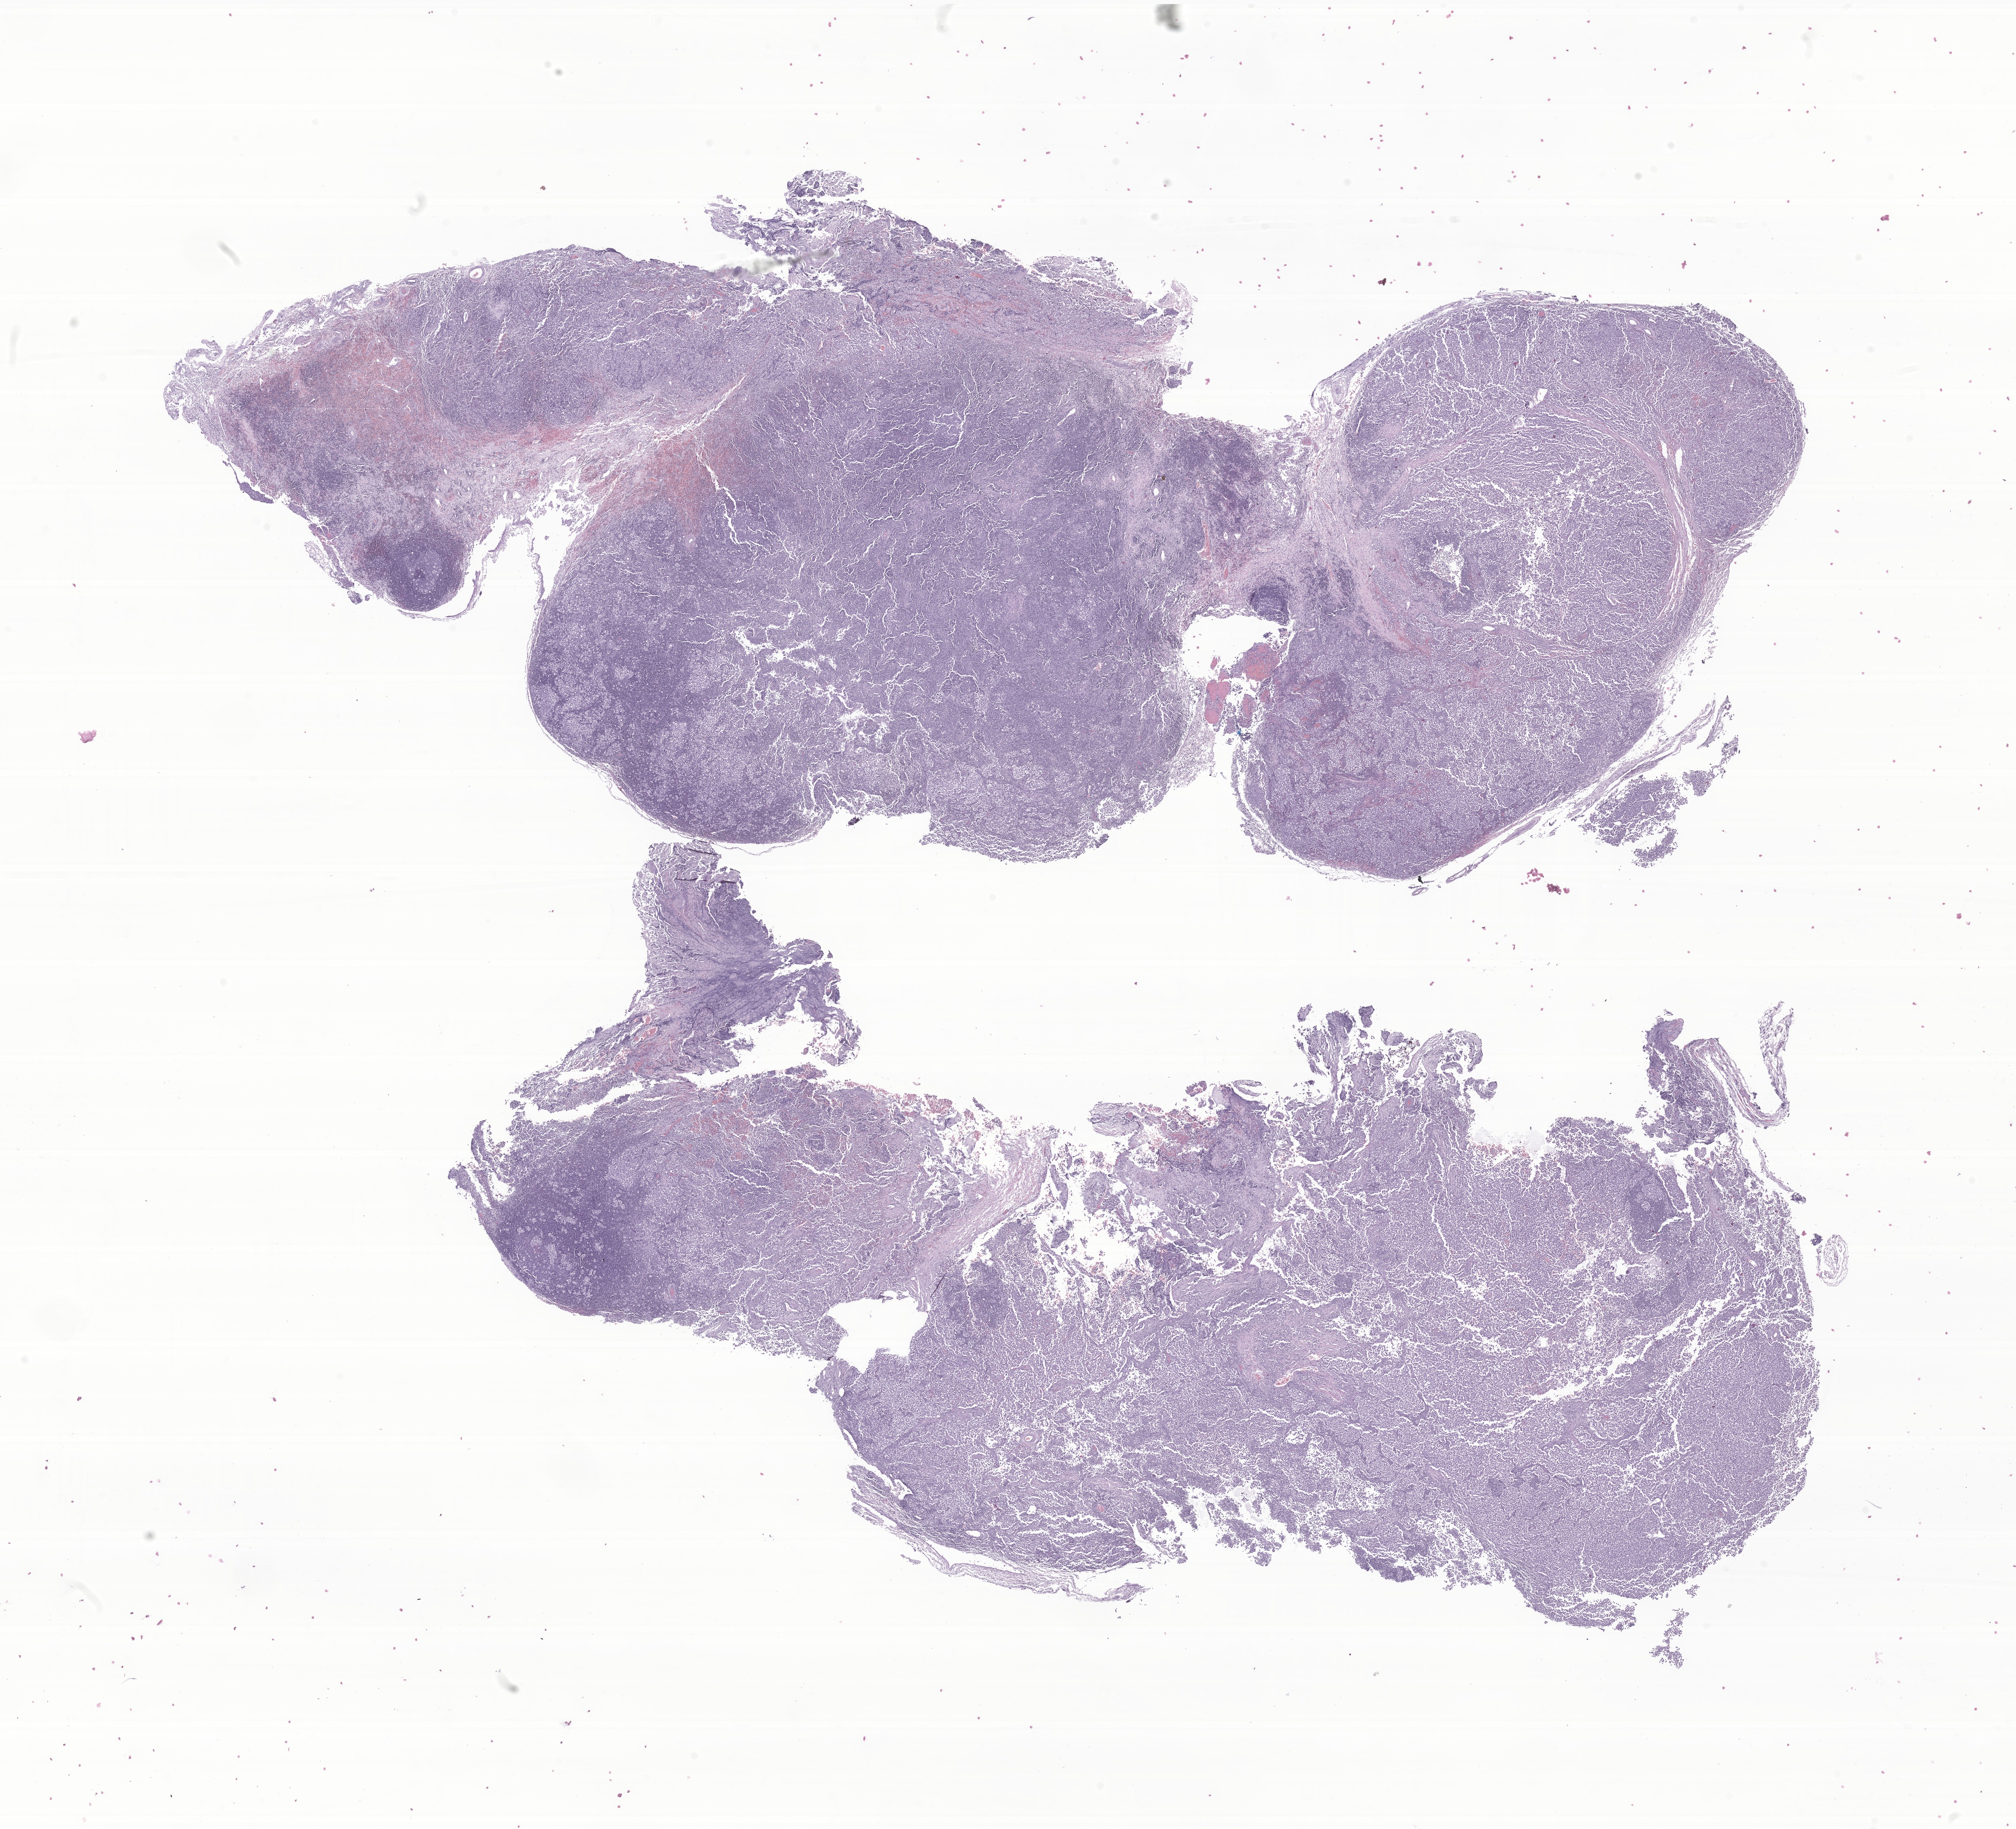
H&E whole-slide image of tumor tissue from the pituitary gland, low-resolution overview of the scanned area, about 22.6 x 20.5 mm. Formalin-fixed, paraffin-embedded (FFPE) tissue. Male patient, age 309 months (25 years 9 months).
* diagnosis (ICD-O-3 morphology term): Germ cell tumor, nonseminomatous